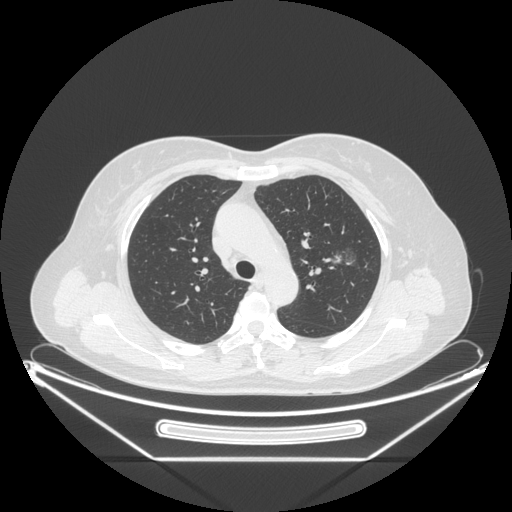
Chest CT, one axial slice; position 153 of 226 along the scan axis; reconstruction kernel STANDARD; 120 kVp; lung window (W 1500 / L -600 HU); 512 × 512 image matrix, field of view 447 × 447 mm. Patient: female, 54 years. Case-level facts recorded for this patient, not image findings: clinical TNM (as recorded): T1c N0 M0; histopathological grade: G1.
Outlined on this slice (bounding box drawn by a radiologist):
- lung tumour (recorded histology: adenocarcinoma): bounding box <325,242,360,278> (left, top, right, bottom; pixels)